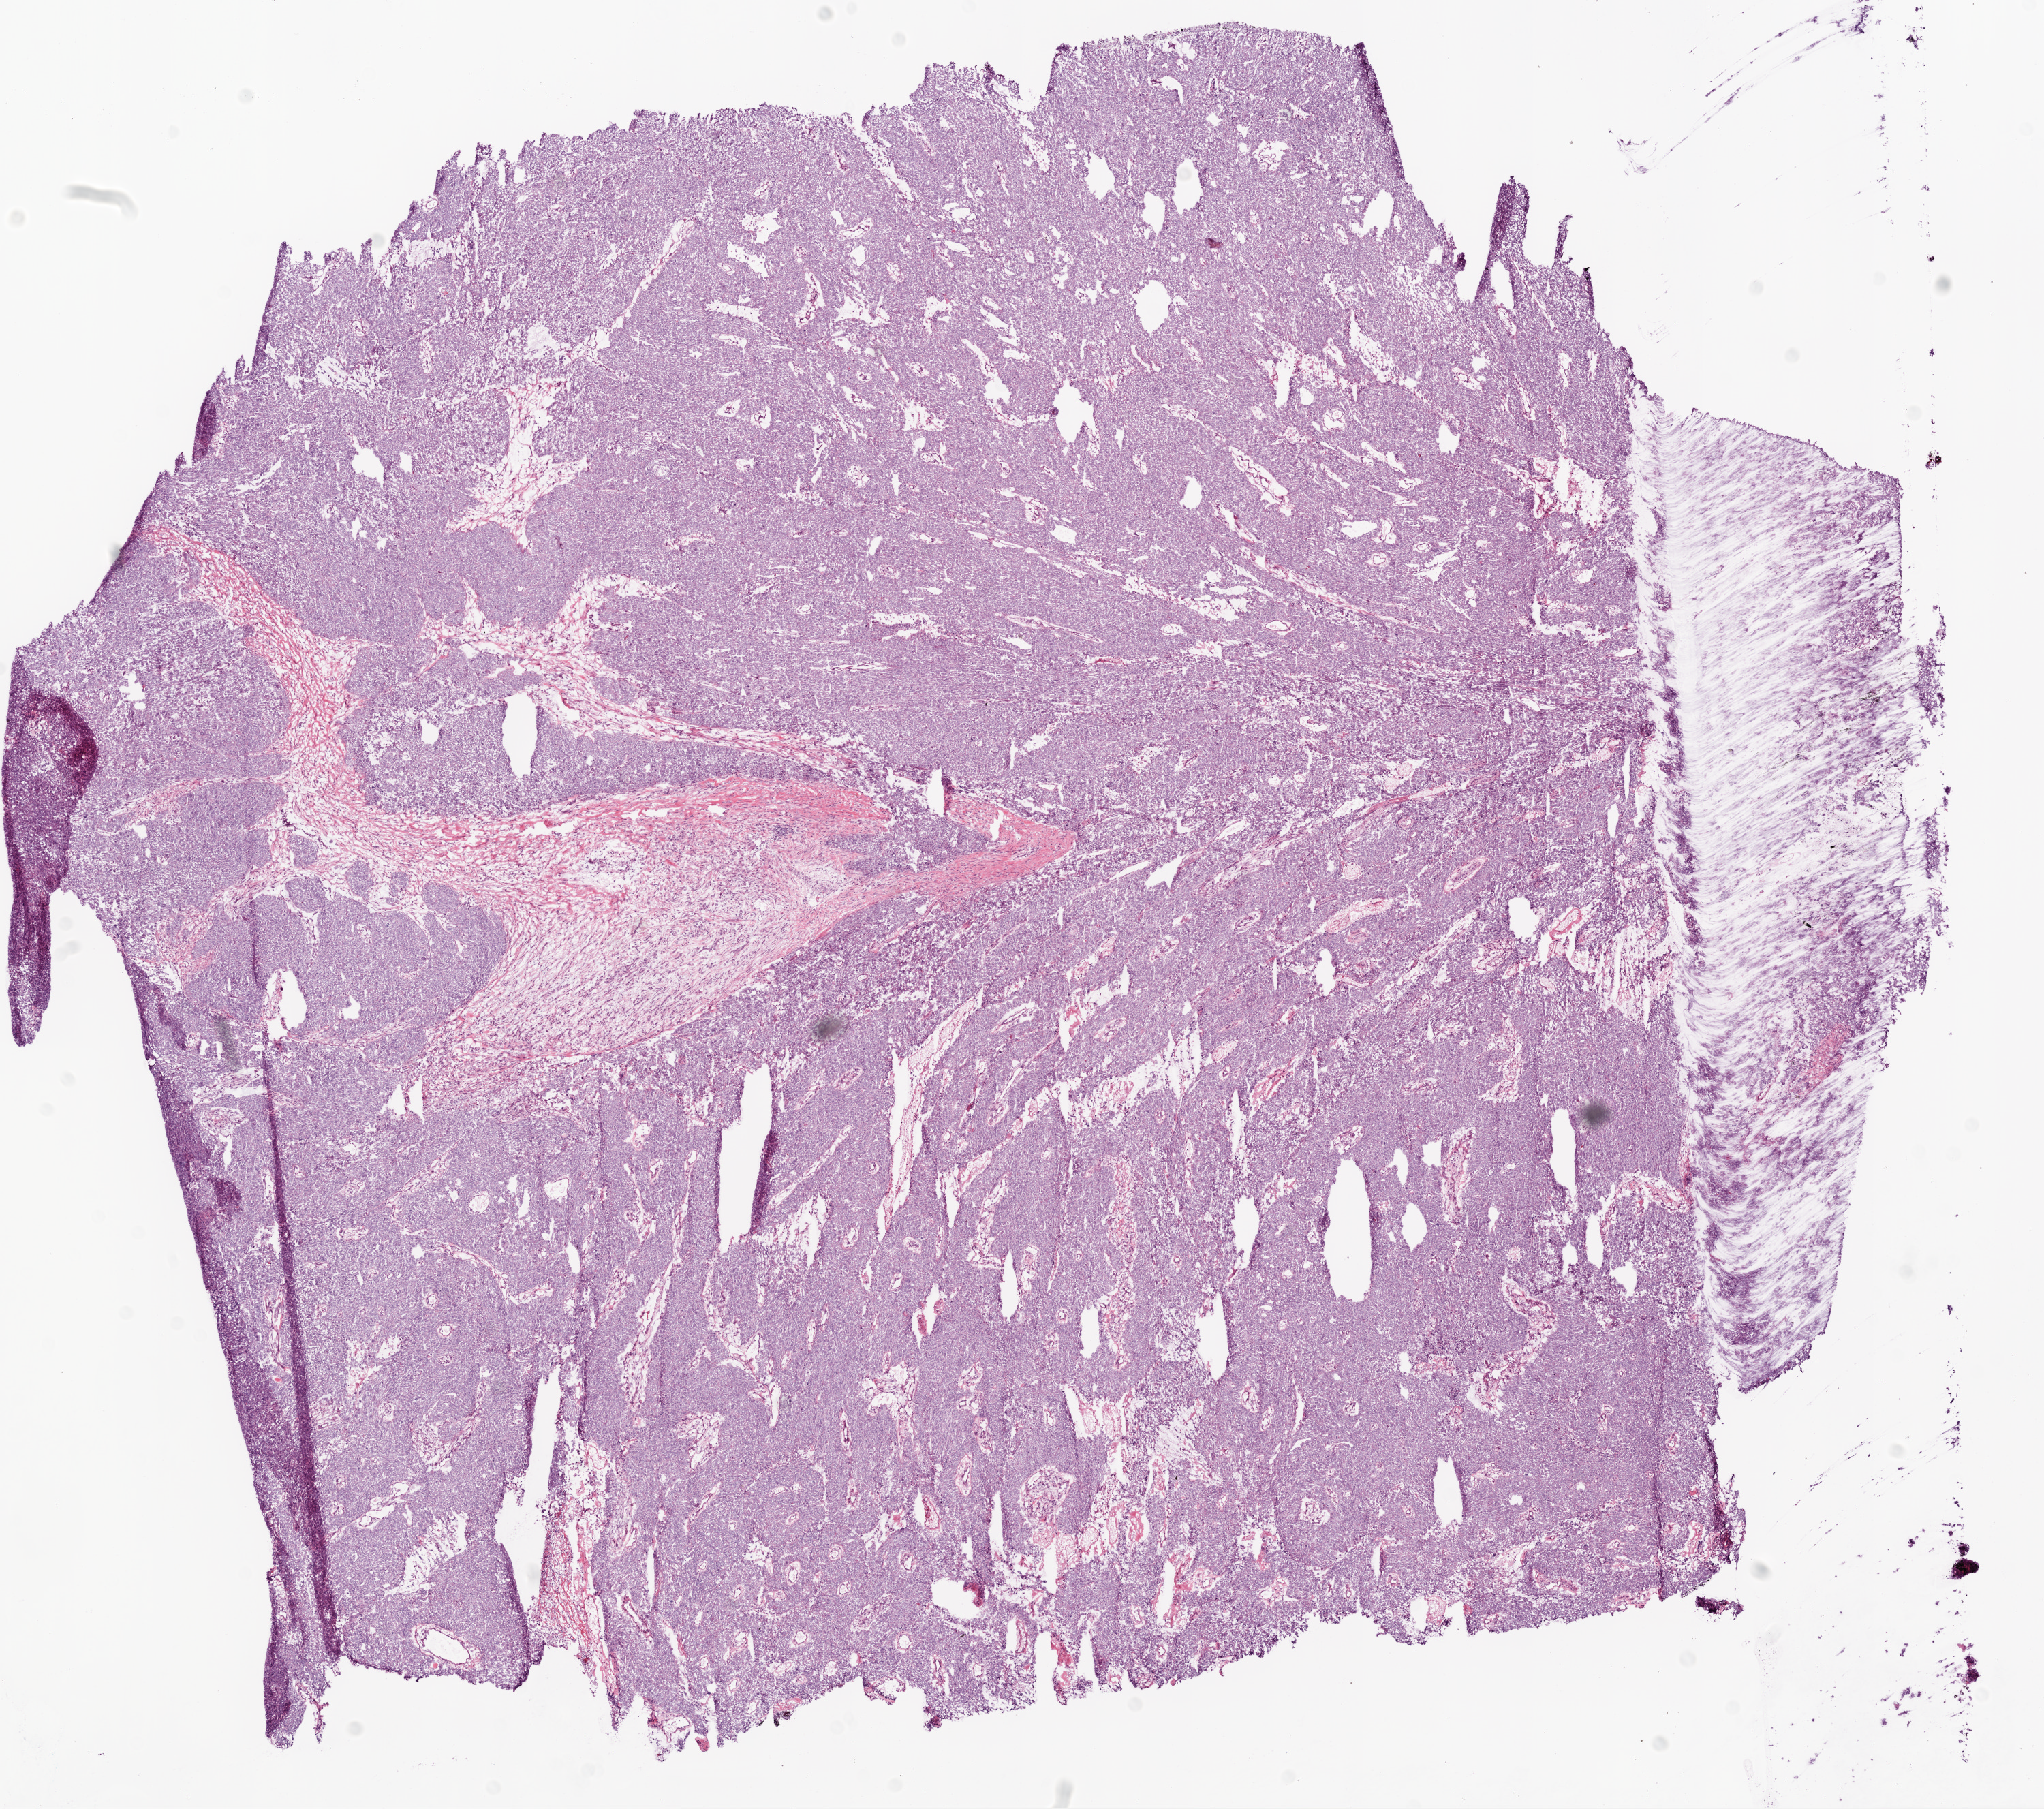
Digitized H&E-stained tissue section (whole slide), shown as a low-resolution overview of the whole scanned area (about 12.0 x 10.7 mm), frozen section from the bottom of the tissue portion, sample: primary tumour, ovary. Female, age 57 years at initial diagnosis. Histologic grade: G3 (poorly differentiated). Composition of this section per pathologist review: tumour cells 94%, tumour nuclei 95%, normal cells 0%, stromal cells 10%, necrosis 1%.
FIGO stage: IIIC. Diagnosis: Serous cystadenocarcinoma, NOS.